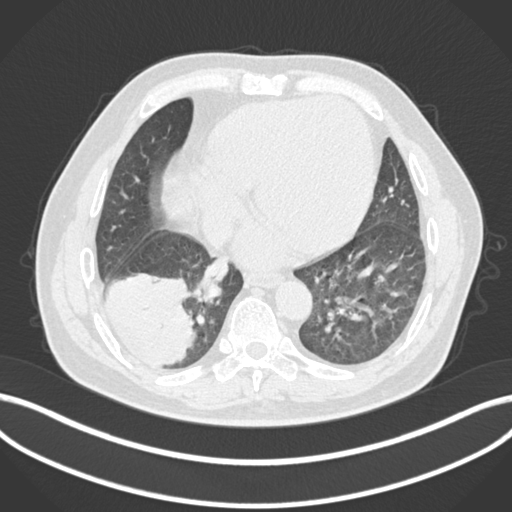
Chest CT, one axial slice. Slice 48 of 200 in the series (ordered by position). Lung window (W 1500 / L -600 HU). 1 mm slice thickness. 512 × 512 image matrix, field of view 400 × 400 mm. Male patient, age 59 years.
Annotated regions visible in this slice (bounding box drawn by a radiologist):
- lung tumour (recorded histology: adenocarcinoma): box from (x=107, y=271) to (x=200, y=371) px